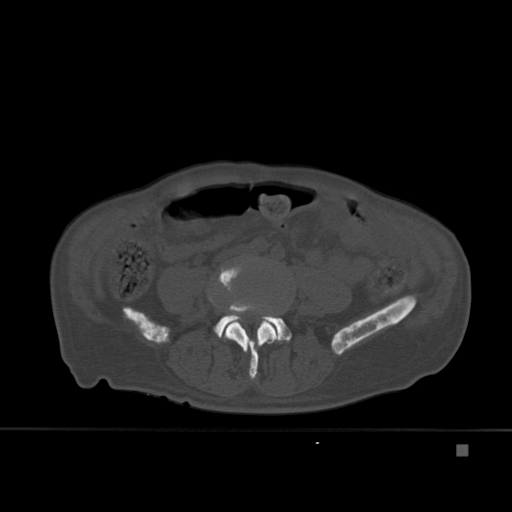
CT including the spine, one axial slice; slice 115 of 451 in the series (ordered by position); bone window (W 1800 / L 400 HU); 1.5 mm slice thickness; 512 × 512 image matrix, field of view 378 × 378 mm. Patient: male, 75 years. Case-level facts recorded for this patient, not image findings: primary cancer: prostate.
Structures marked on this image (semi-automatic segmentation, software-assisted and operator-edited):
- L4 vertebra: bounding box [x1, y1, x2, y2] px = [210, 267, 279, 379]
- L5 vertebra: [214, 314, 292, 344]
- T7 vertebra: [213, 313, 281, 331]